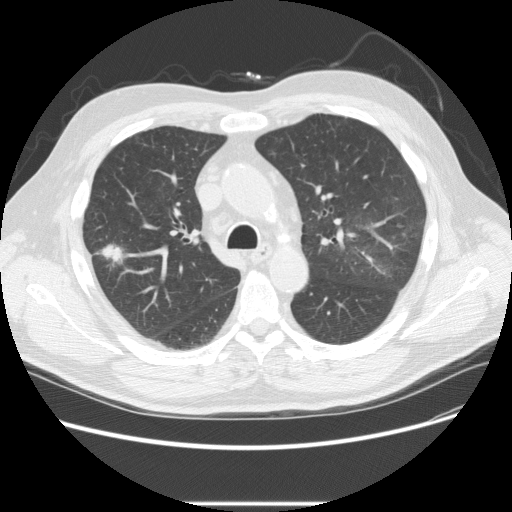
Low-dose screening chest CT, one axial slice; position 156 of 233 along the scan axis; reconstruction kernel STANDARD; lung window (W 1500 / L -600 HU); 2.5 mm slice thickness; 512 × 512 image matrix, field of view 380 × 380 mm.
Structures marked on this image (outlined manually by an expert reader):
- lesion 2 (tumor, upper lobe of right lung): box from (x=99, y=244) to (x=129, y=264) px